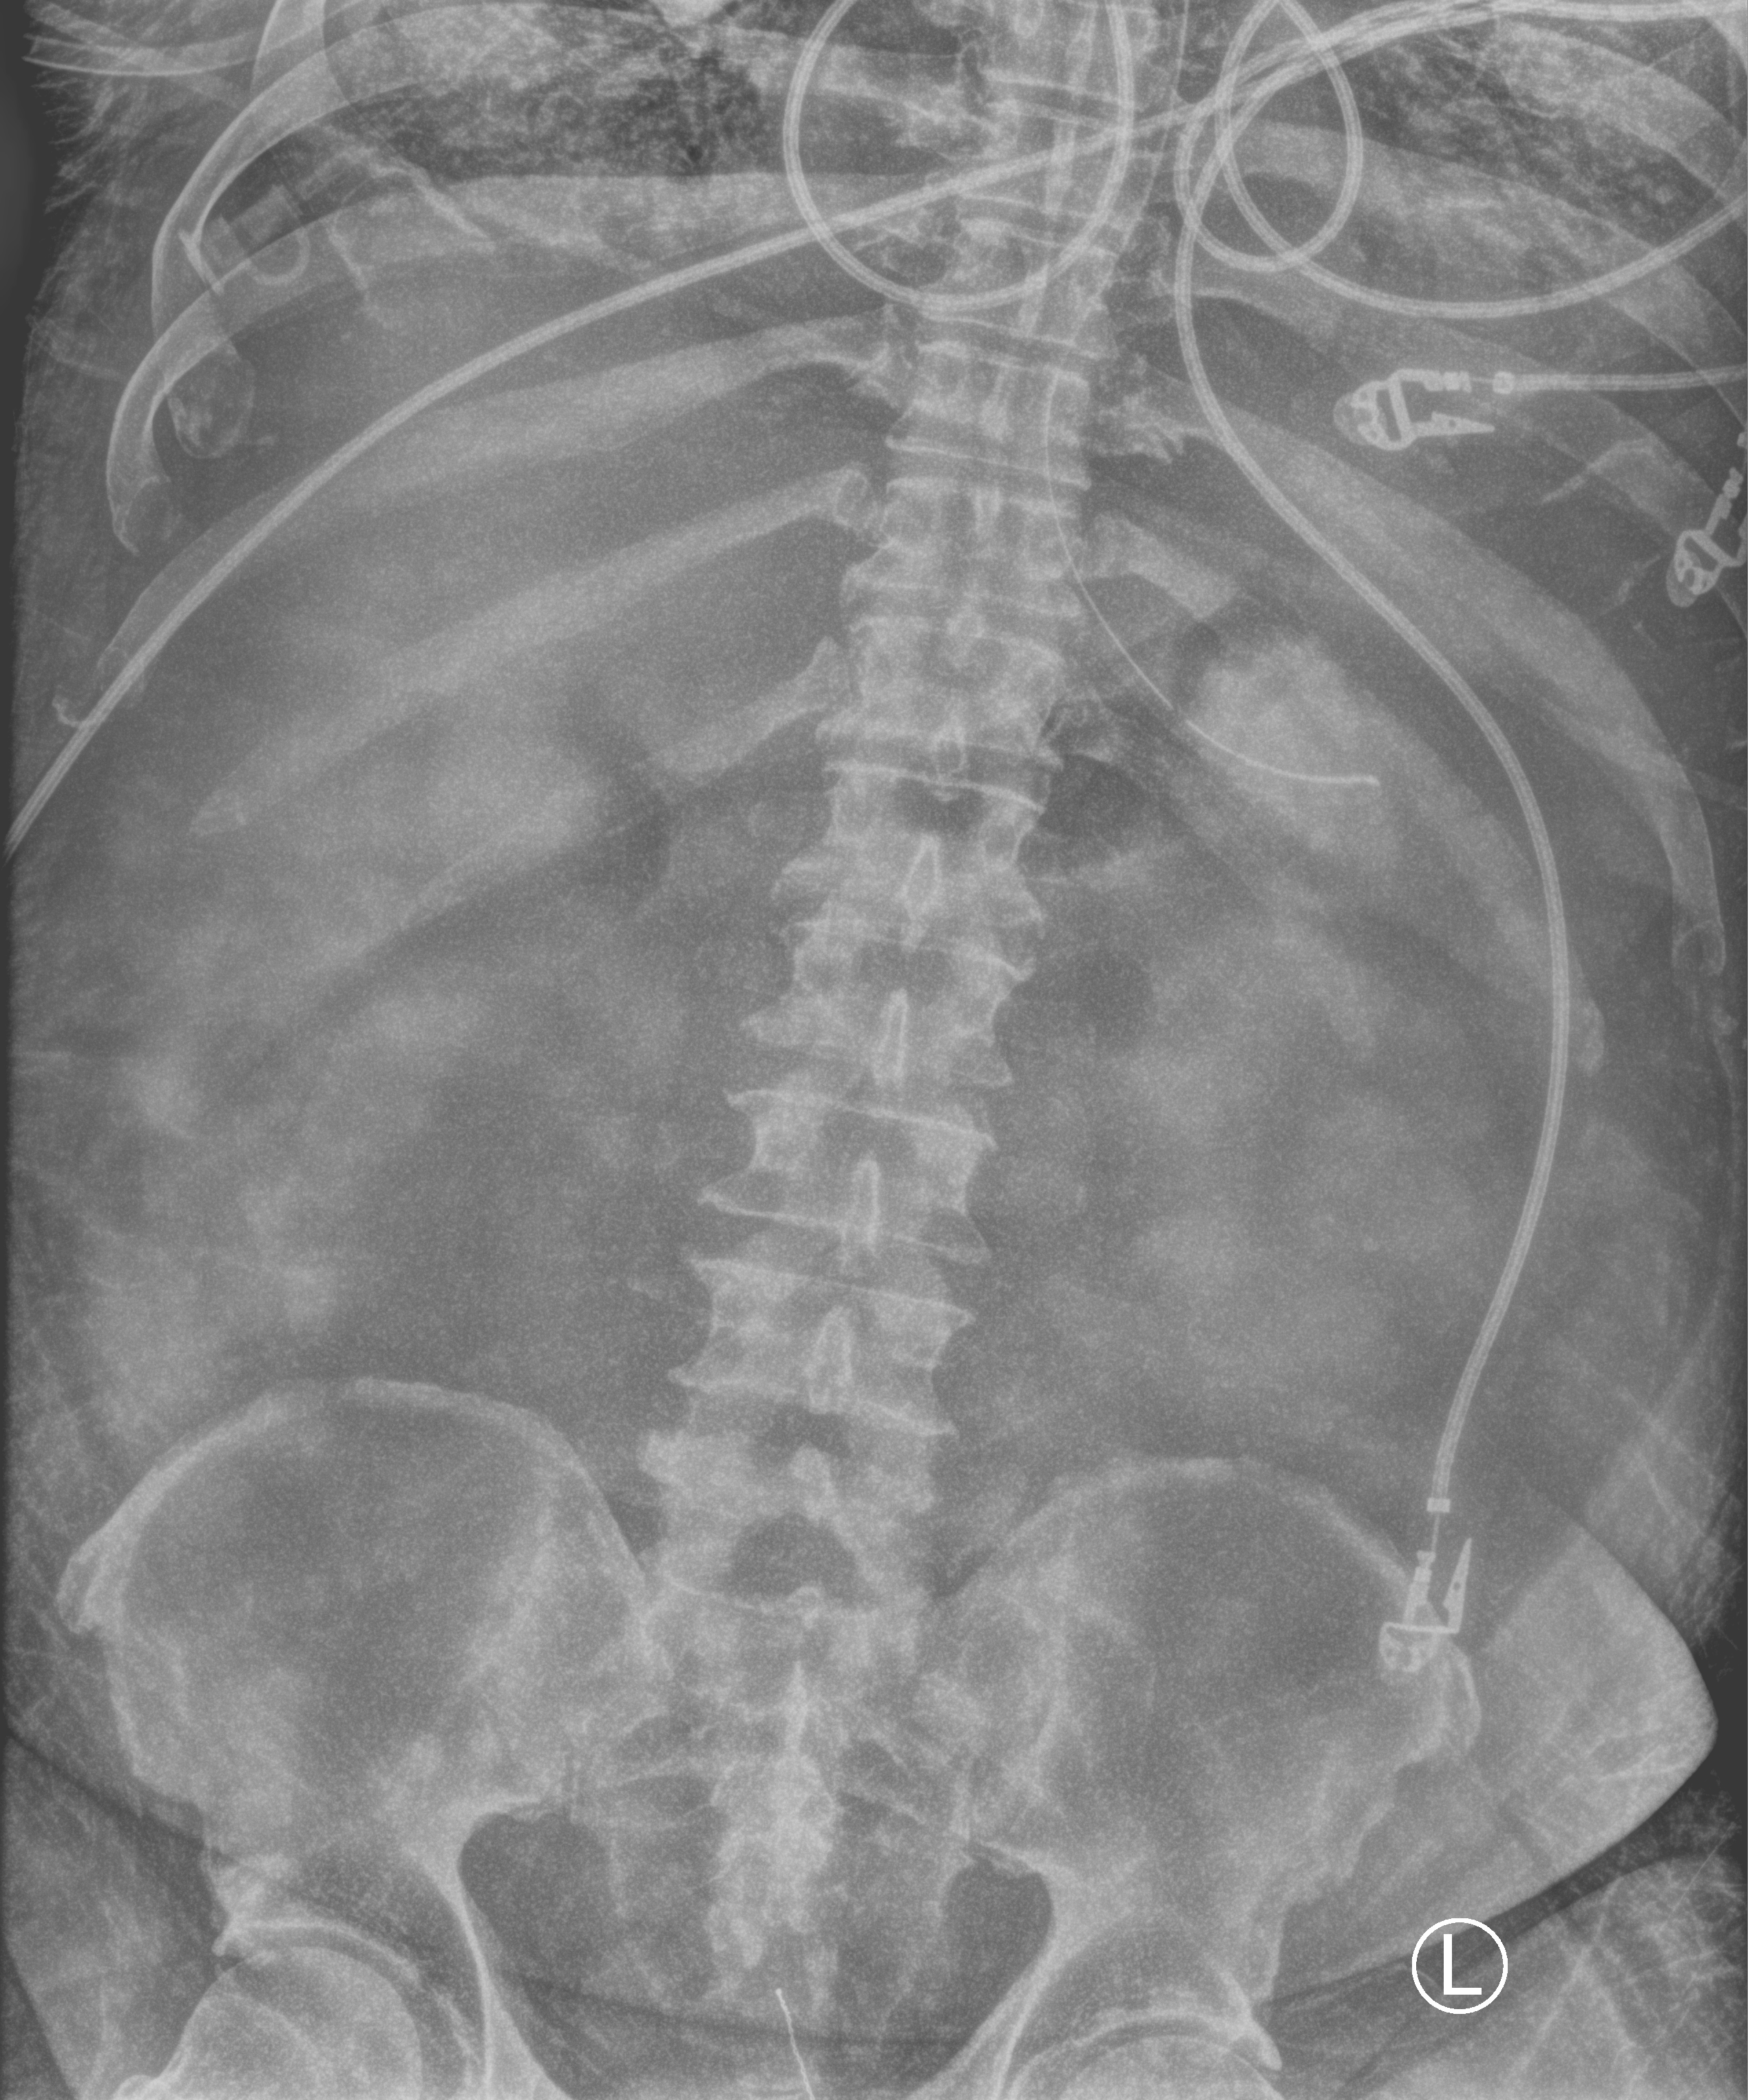
Abdomen X-ray (portable). Patient hospitalised with COVID-19; male, aged 60–74 years.
Hospital-stay facts (about this admission, not read from this image; timing relative to this image not recorded):
- chronic kidney disease (admission record): no